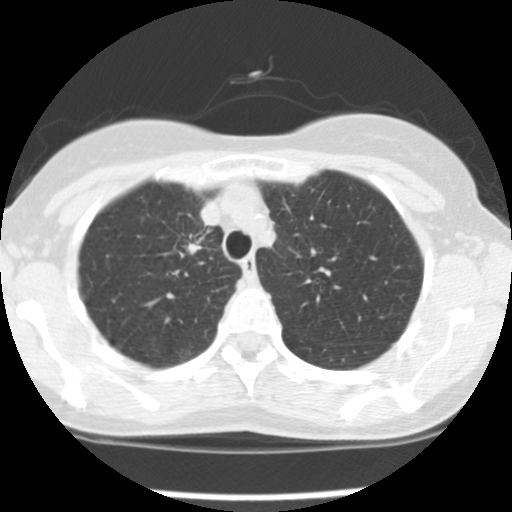
Low-dose screening chest CT, one axial slice. Slice 121 of 157 in the series (ordered by position). 120 kVp. Lung window (W 1500 / L -600 HU). 2.5 mm slice thickness. 512 × 512 image matrix, field of view 282 × 282 mm.
Structures marked on this image (manually delineated by an expert):
- lesion 1 (tumor, upper lobe of right lung): bounding box <187,243,202,255> (left, top, right, bottom; pixels)